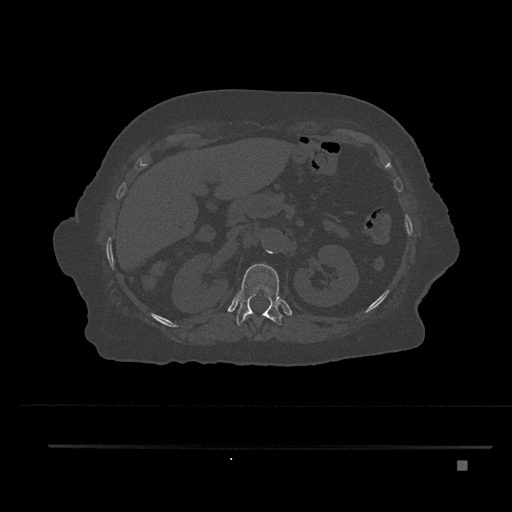
CT including the spine, one axial slice; slice 269 of 797 in the series (ordered by position); reconstruction kernel Br40s/3; 120 kVp; bone window (W 1800 / L 400 HU); 0.5 mm slice thickness; 512 × 512 image matrix, field of view 437 × 437 mm. Female patient, age 76 years. From the clinical record (not read from this slice): primary cancer: lung.
Outlined on this slice (semi-automatic segmentation, software-assisted and operator-edited):
- T11 vertebra: bounding box <244,314,252,321> (left, top, right, bottom; pixels)
- T12 vertebra: <236,264,282,326>